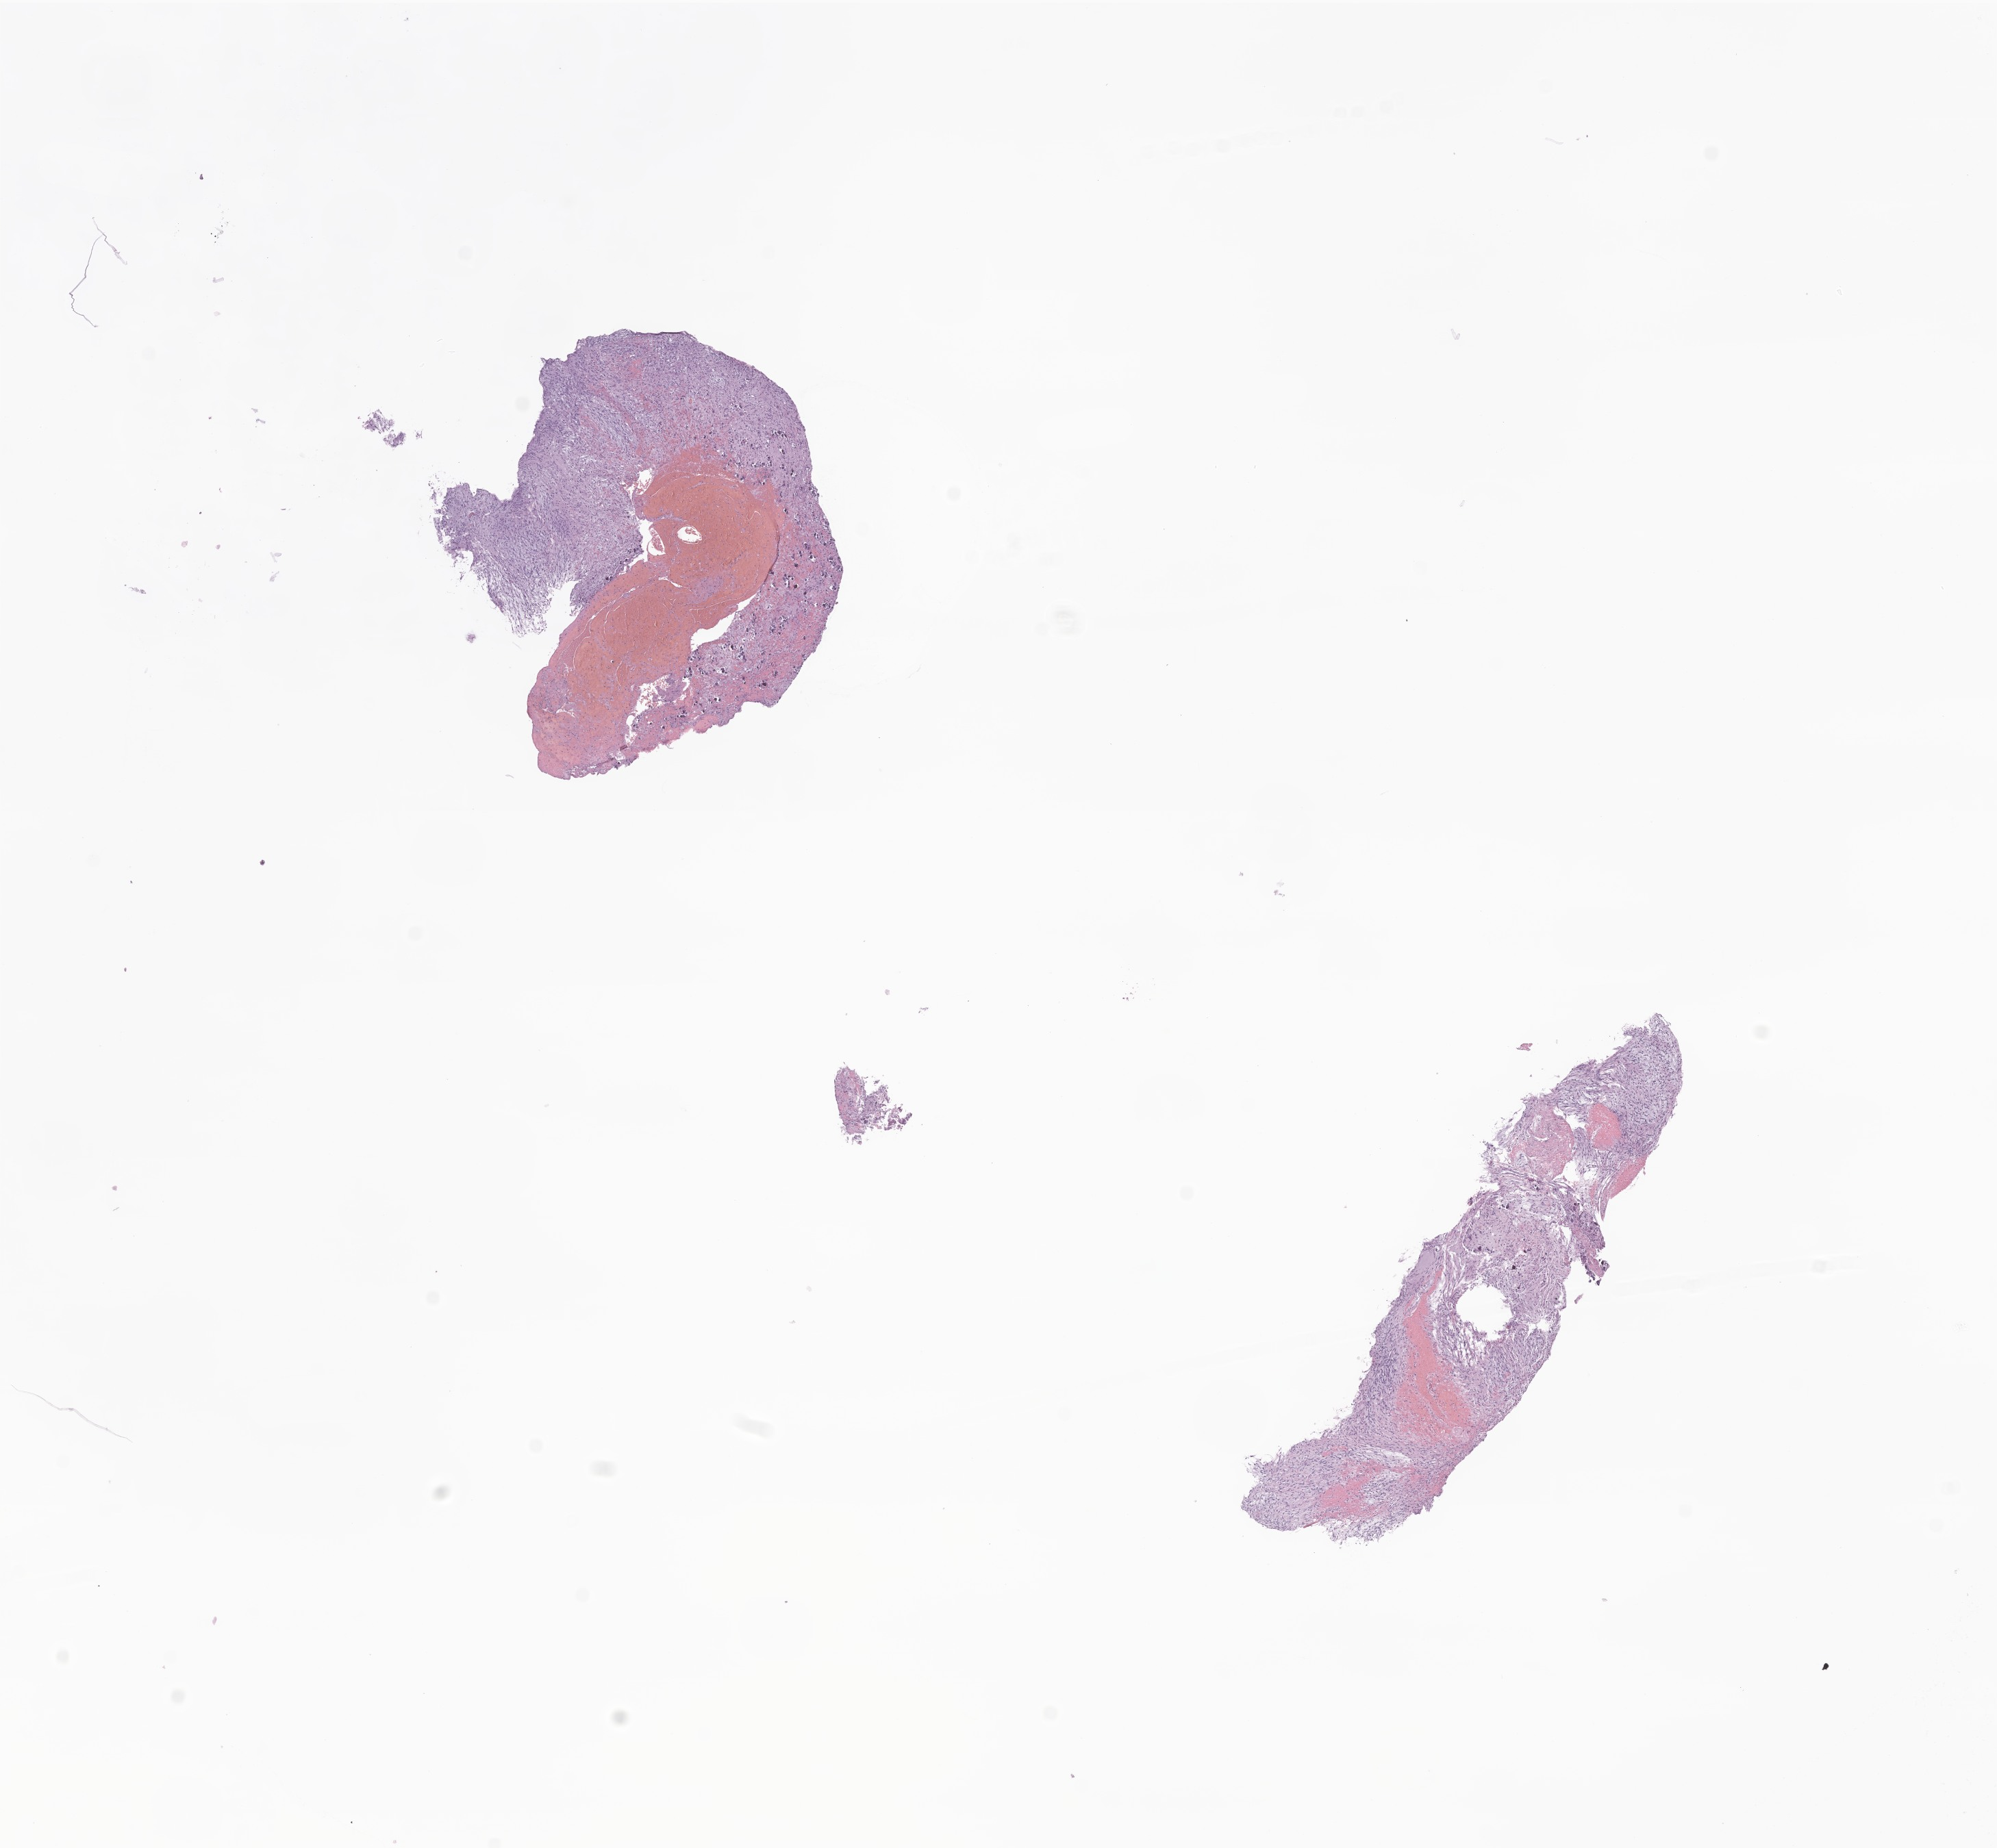
Whole-slide image, hematoxylin and eosin (H&E) stain of tumor tissue from the brain — shown as a low-resolution overview of the whole scanned area (about 12.3 x 11.4 mm), FFPE section. Patient male; age 40 months (3 years 4 months).
• recorded diagnosis: Glioma, malignant